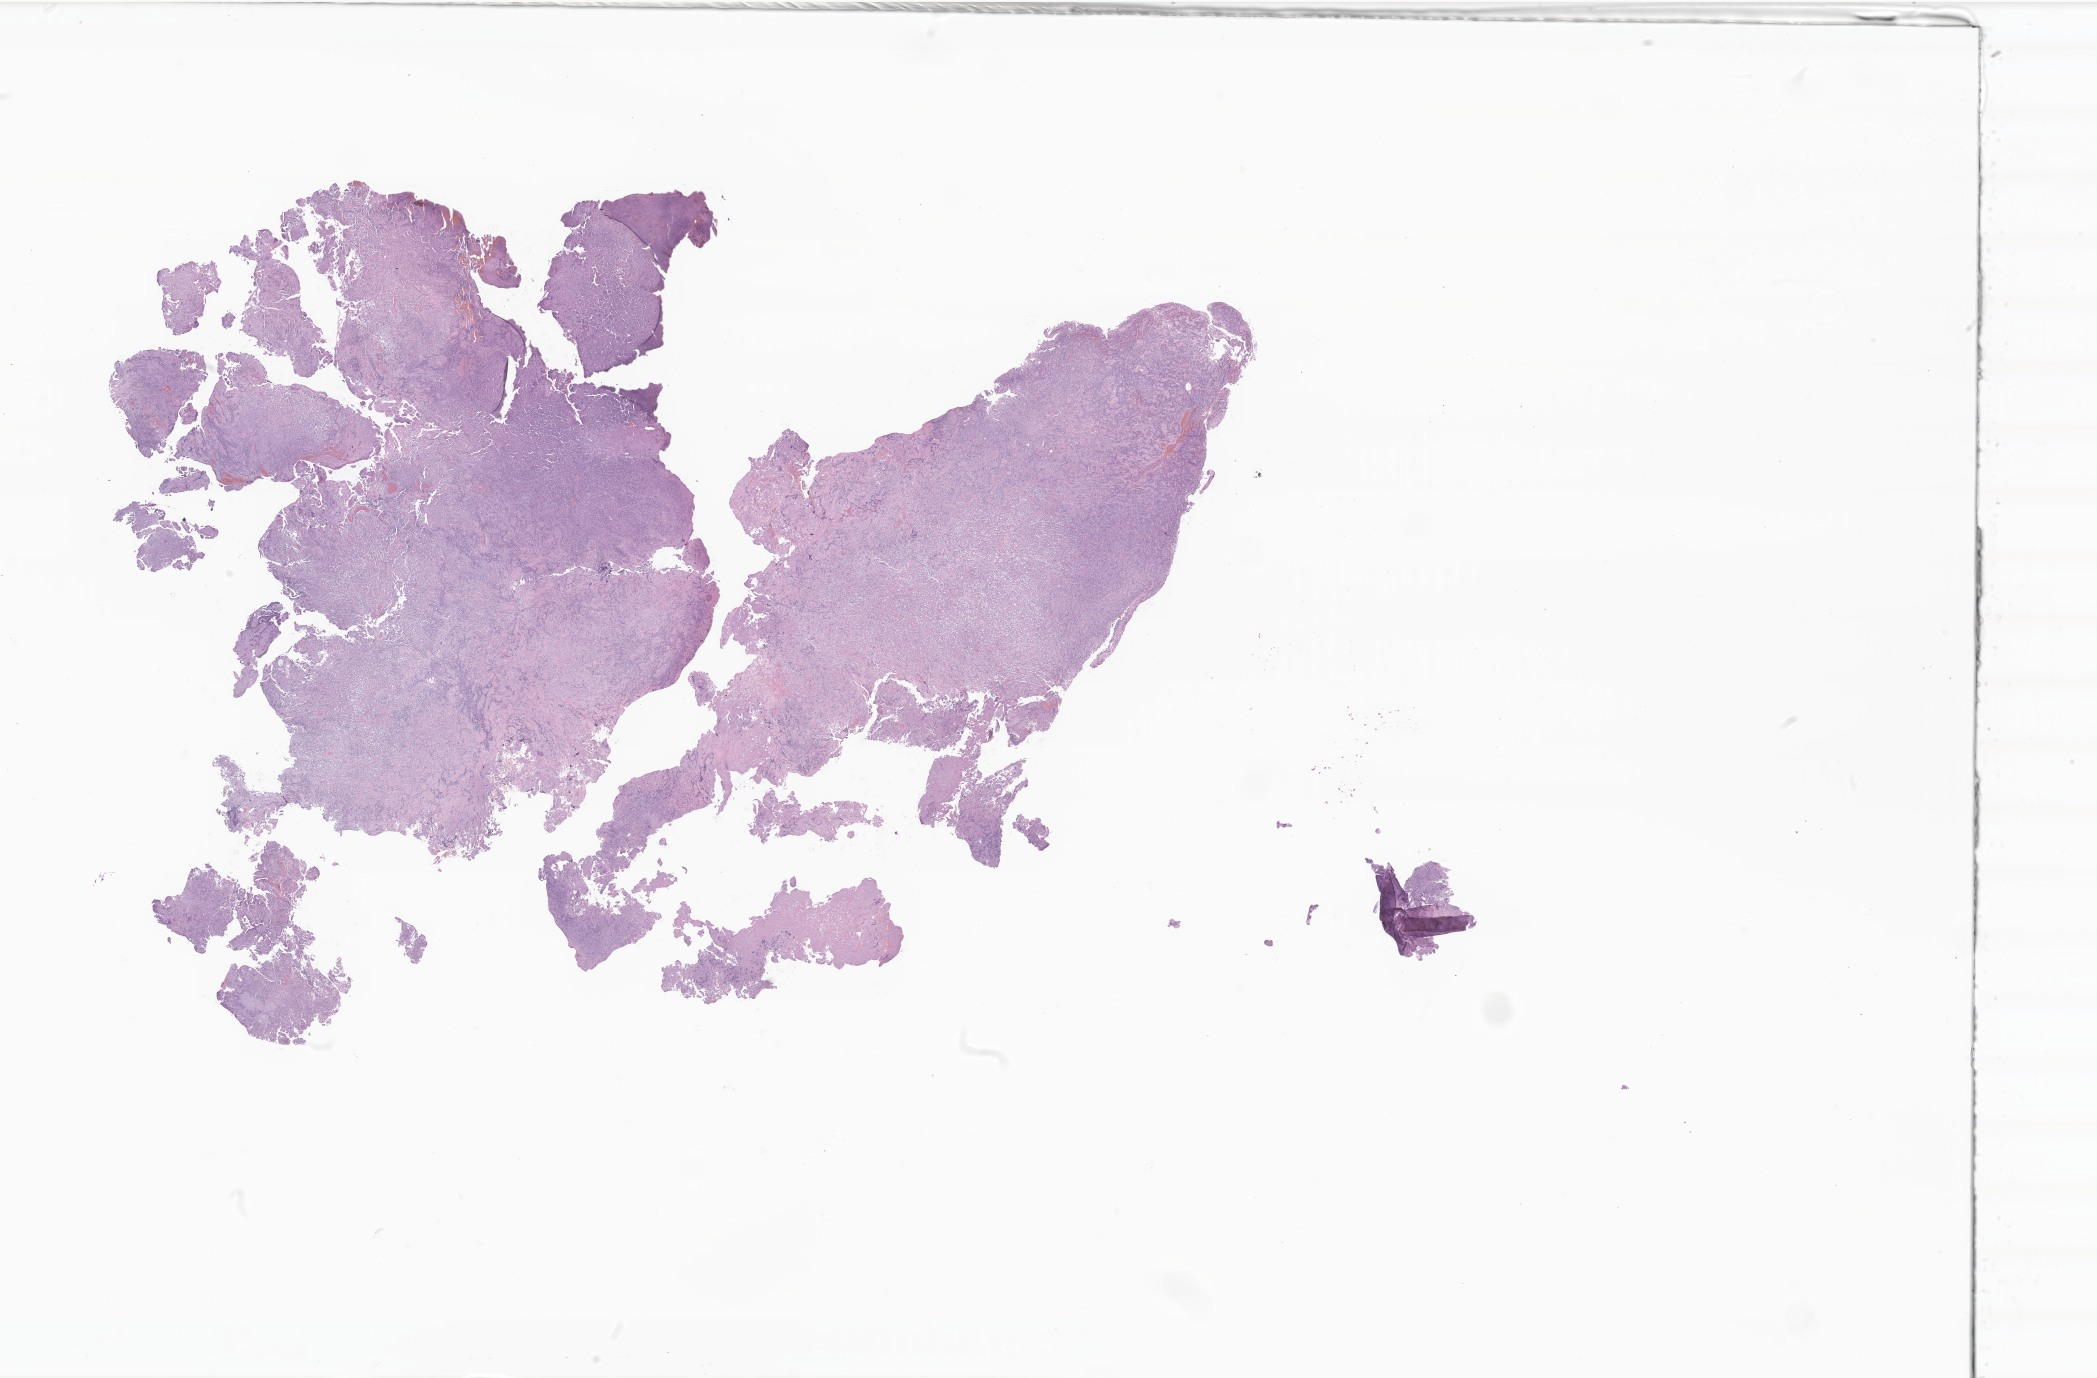
Hematoxylin and eosin (H&E) whole-slide image of tumor tissue from the brain — low-resolution overview of the scanned area, about 35.4 x 23.2 mm, formalin-fixed paraffin-embedded section. Patient female; age 113 months (9 years 5 months).
* diagnosis (ICD-O-3 morphology term): Astroblastoma